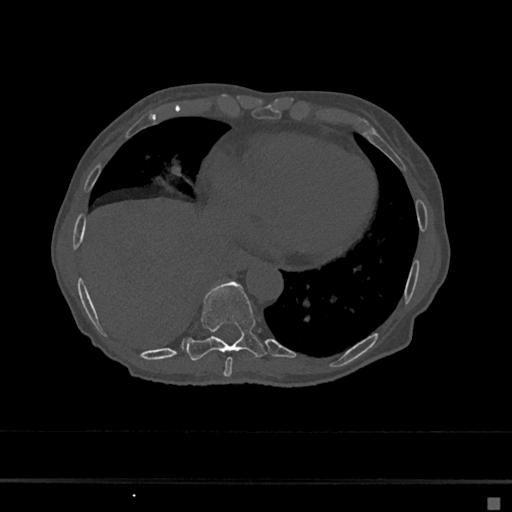
CT including the spine, one axial slice. Slice 278 of 797 in the series (ordered by position). Reconstruction kernel Br40s/3. 120 kVp. Bone window (W 1800 / L 400 HU). 0.5 mm slice thickness. 512 × 512 image matrix, field of view 360 × 360 mm. Patient: female, 68 years. Case-level facts recorded for this patient, not image findings: primary cancer: renal.
Annotated regions visible in this slice (semi-automatic segmentation, software-assisted and operator-edited):
- T8 vertebra: bounding box (x1, y1, x2, y2) in pixels: (224, 357, 233, 377)
- T9 vertebra: (187, 282, 265, 361)